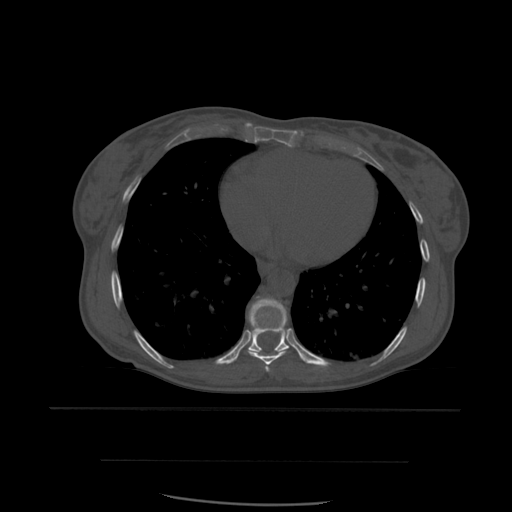
CT including the spine, one axial slice. Slice 347 of 574 in the series (ordered by position). Bone window (W 1800 / L 400 HU). 1.25 mm slice thickness. 512 × 512 image matrix, field of view 392 × 392 mm. Patient age 48 years. Case-level facts recorded for this patient, not image findings: primary cancer: lung.
Structures marked on this image (semi-automatic segmentation, software-assisted and operator-edited):
- T7 vertebra: bounding box [x1, y1, x2, y2] px = [266, 367, 269, 370]
- T8 vertebra: [247, 297, 287, 372]
- T9 vertebra: [232, 297, 314, 365]